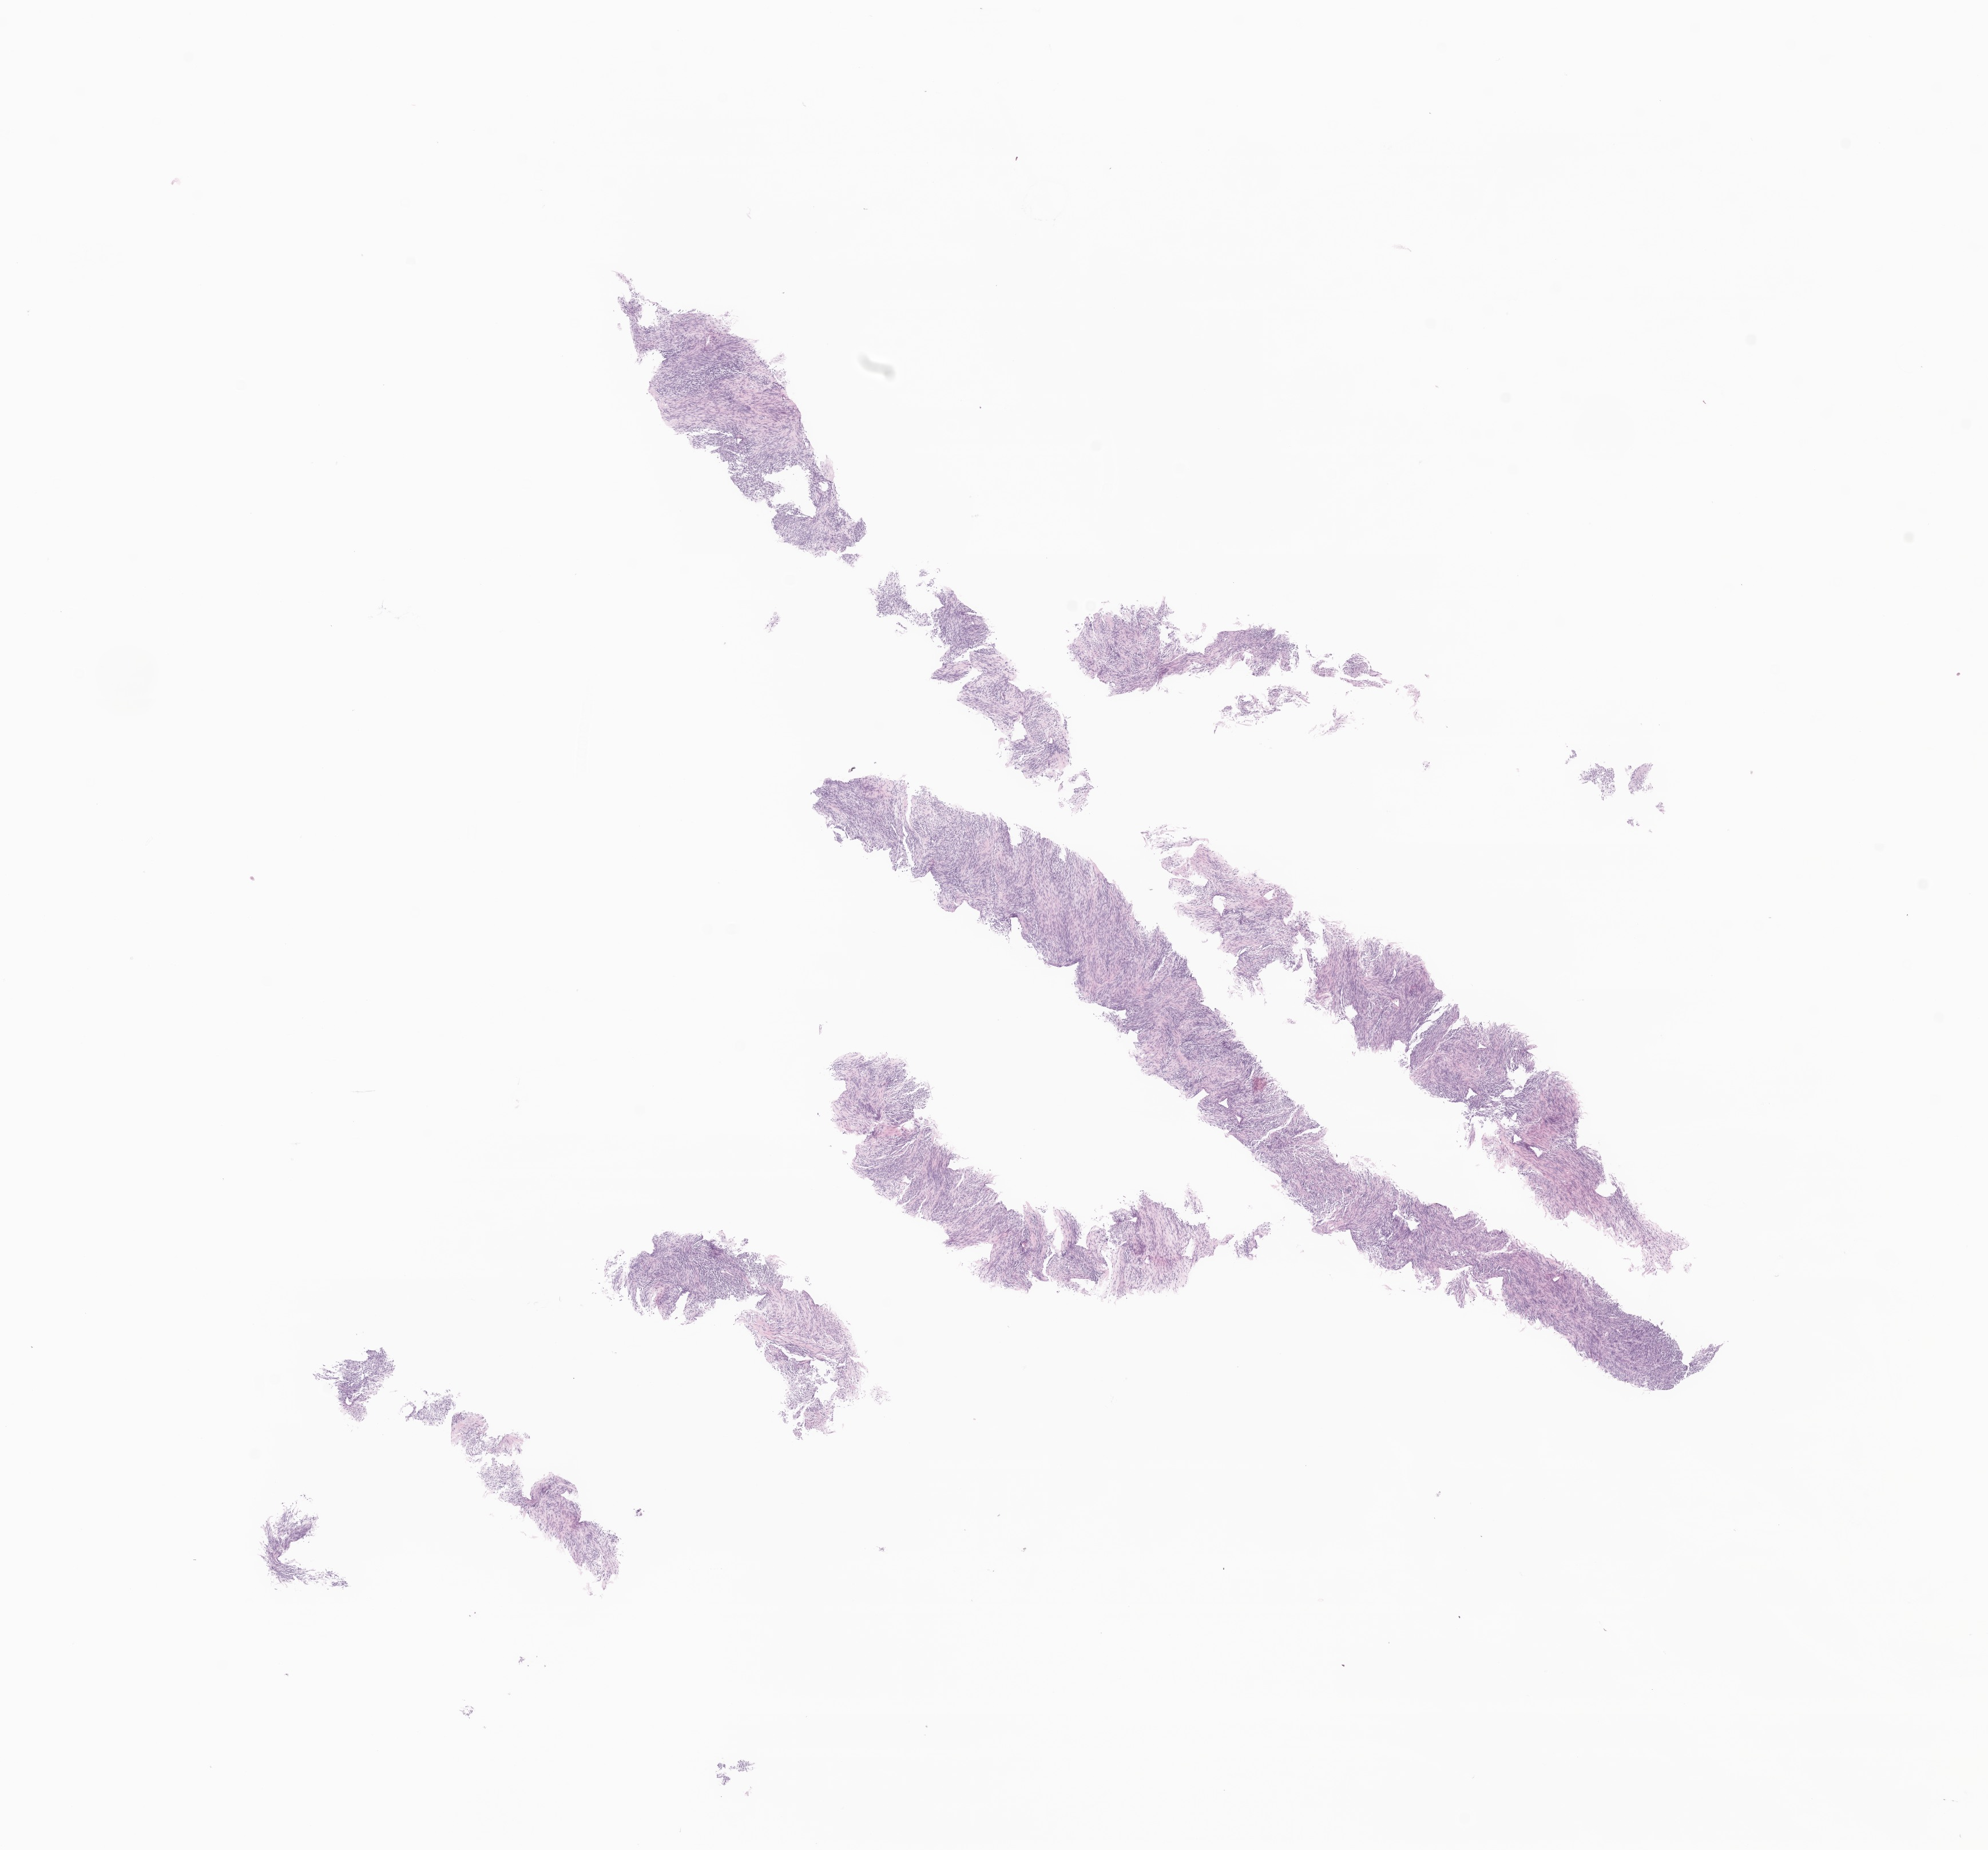
Digitized hematoxylin and eosin (H&E)-stained section of tumor tissue from the long bone of lower limb — low-resolution overview of the scanned area, about 14.7 x 13.6 mm. Formalin-fixed, paraffin-embedded (FFPE) tissue. Patient female; age 185 months.
• diagnosis (ICD-O-3 morphology term): Synovial sarcoma, NOS